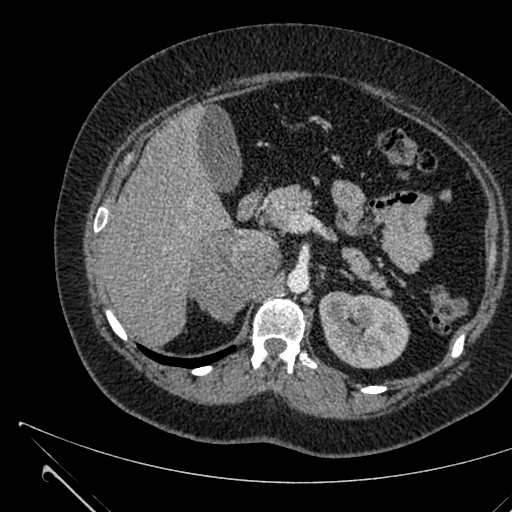
Contrast-enhanced abdominal CT, one axial slice; intravenous contrast given; soft-tissue window (W 400 / L 40 HU); 512 × 512 image matrix, field of view 376 × 376 mm. Patient: female, 36 years. From the clinical record (not read from this slice): diagnosis: adrenocortical carcinoma; tumour side: right adrenal; tumour size at pathology: 10 cm; Ki-67 index: 20 %; stage (as recorded): 4.
Outlined on this slice (semi-automatic segmentation, software-assisted and operator-edited):
- mass: bounding box (x1, y1, x2, y2) in pixels: (191, 231, 277, 320)